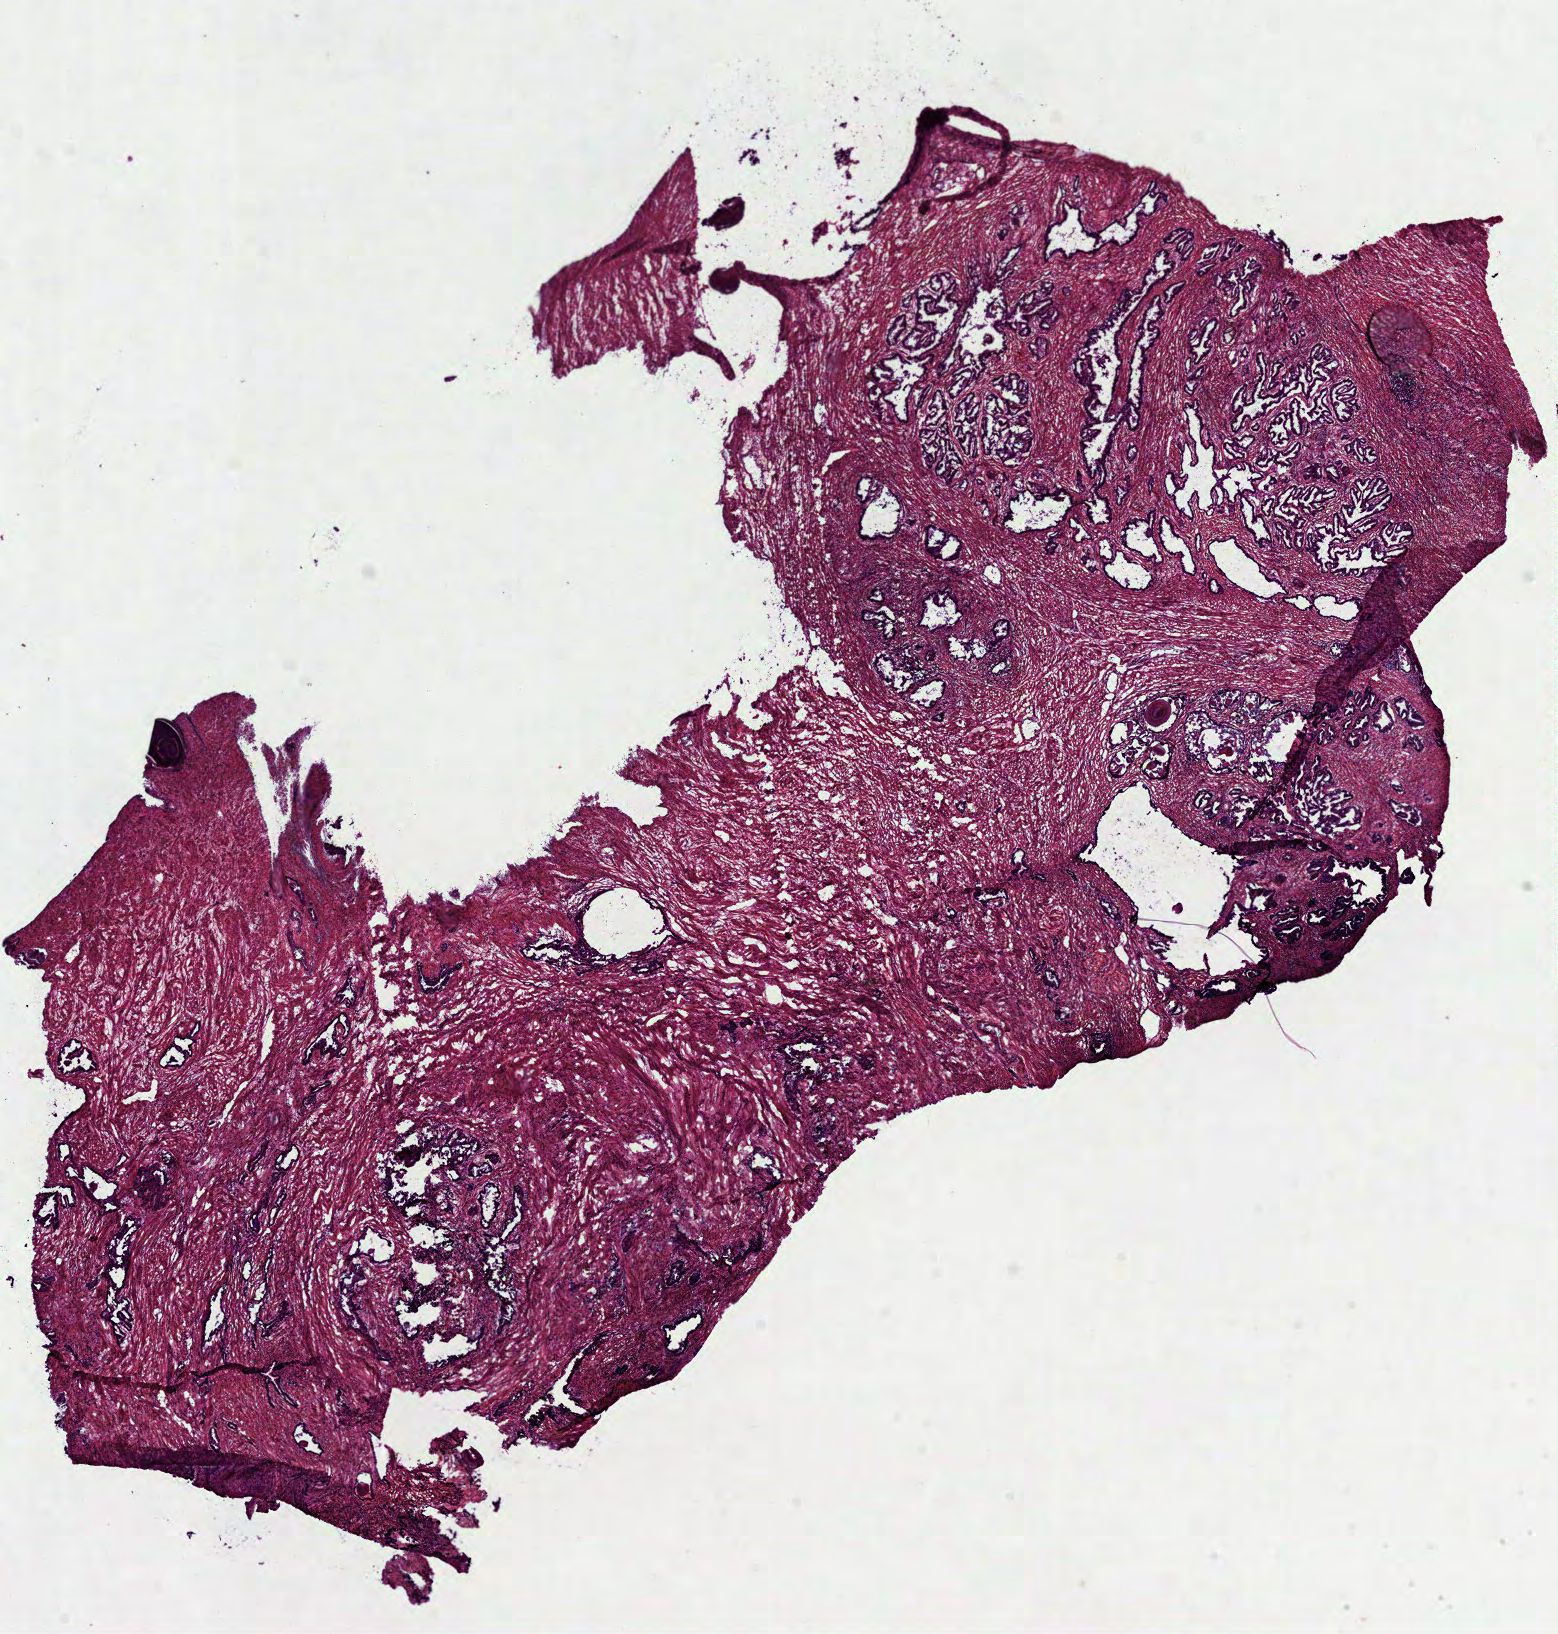
Digitized H&E tissue section (whole slide) — shown as a low-resolution overview of the whole scanned area (about 12.6 x 13.2 mm, from a 40x scan). Frozen section. Sample: solid tissue normal (non-tumour tissue), prostate. Male, age 72 years at initial diagnosis.
This section: solid tissue normal sample (biorepository sample class). Patient diagnosis: Acinar cell carcinoma (prostate gland).